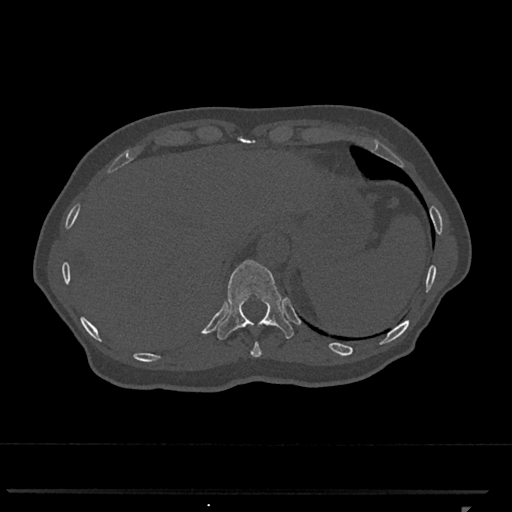
CT including the spine, one axial slice. Position 529 of 793 along the scan axis. Reconstruction kernel Br40s/3. 120 kVp. Bone window (W 1800 / L 400 HU). 0.5 mm slice thickness. 512 × 512 image matrix, field of view 380 × 380 mm. Female patient, age 62 years. Case-level facts recorded for this patient, not image findings: primary cancer: renal.
Annotated regions visible in this slice (semi-automatically segmented with operator editing):
- T10 vertebra: bounding box <250,341,262,357> (left, top, right, bottom; pixels)
- T11 vertebra: <217,260,294,340>